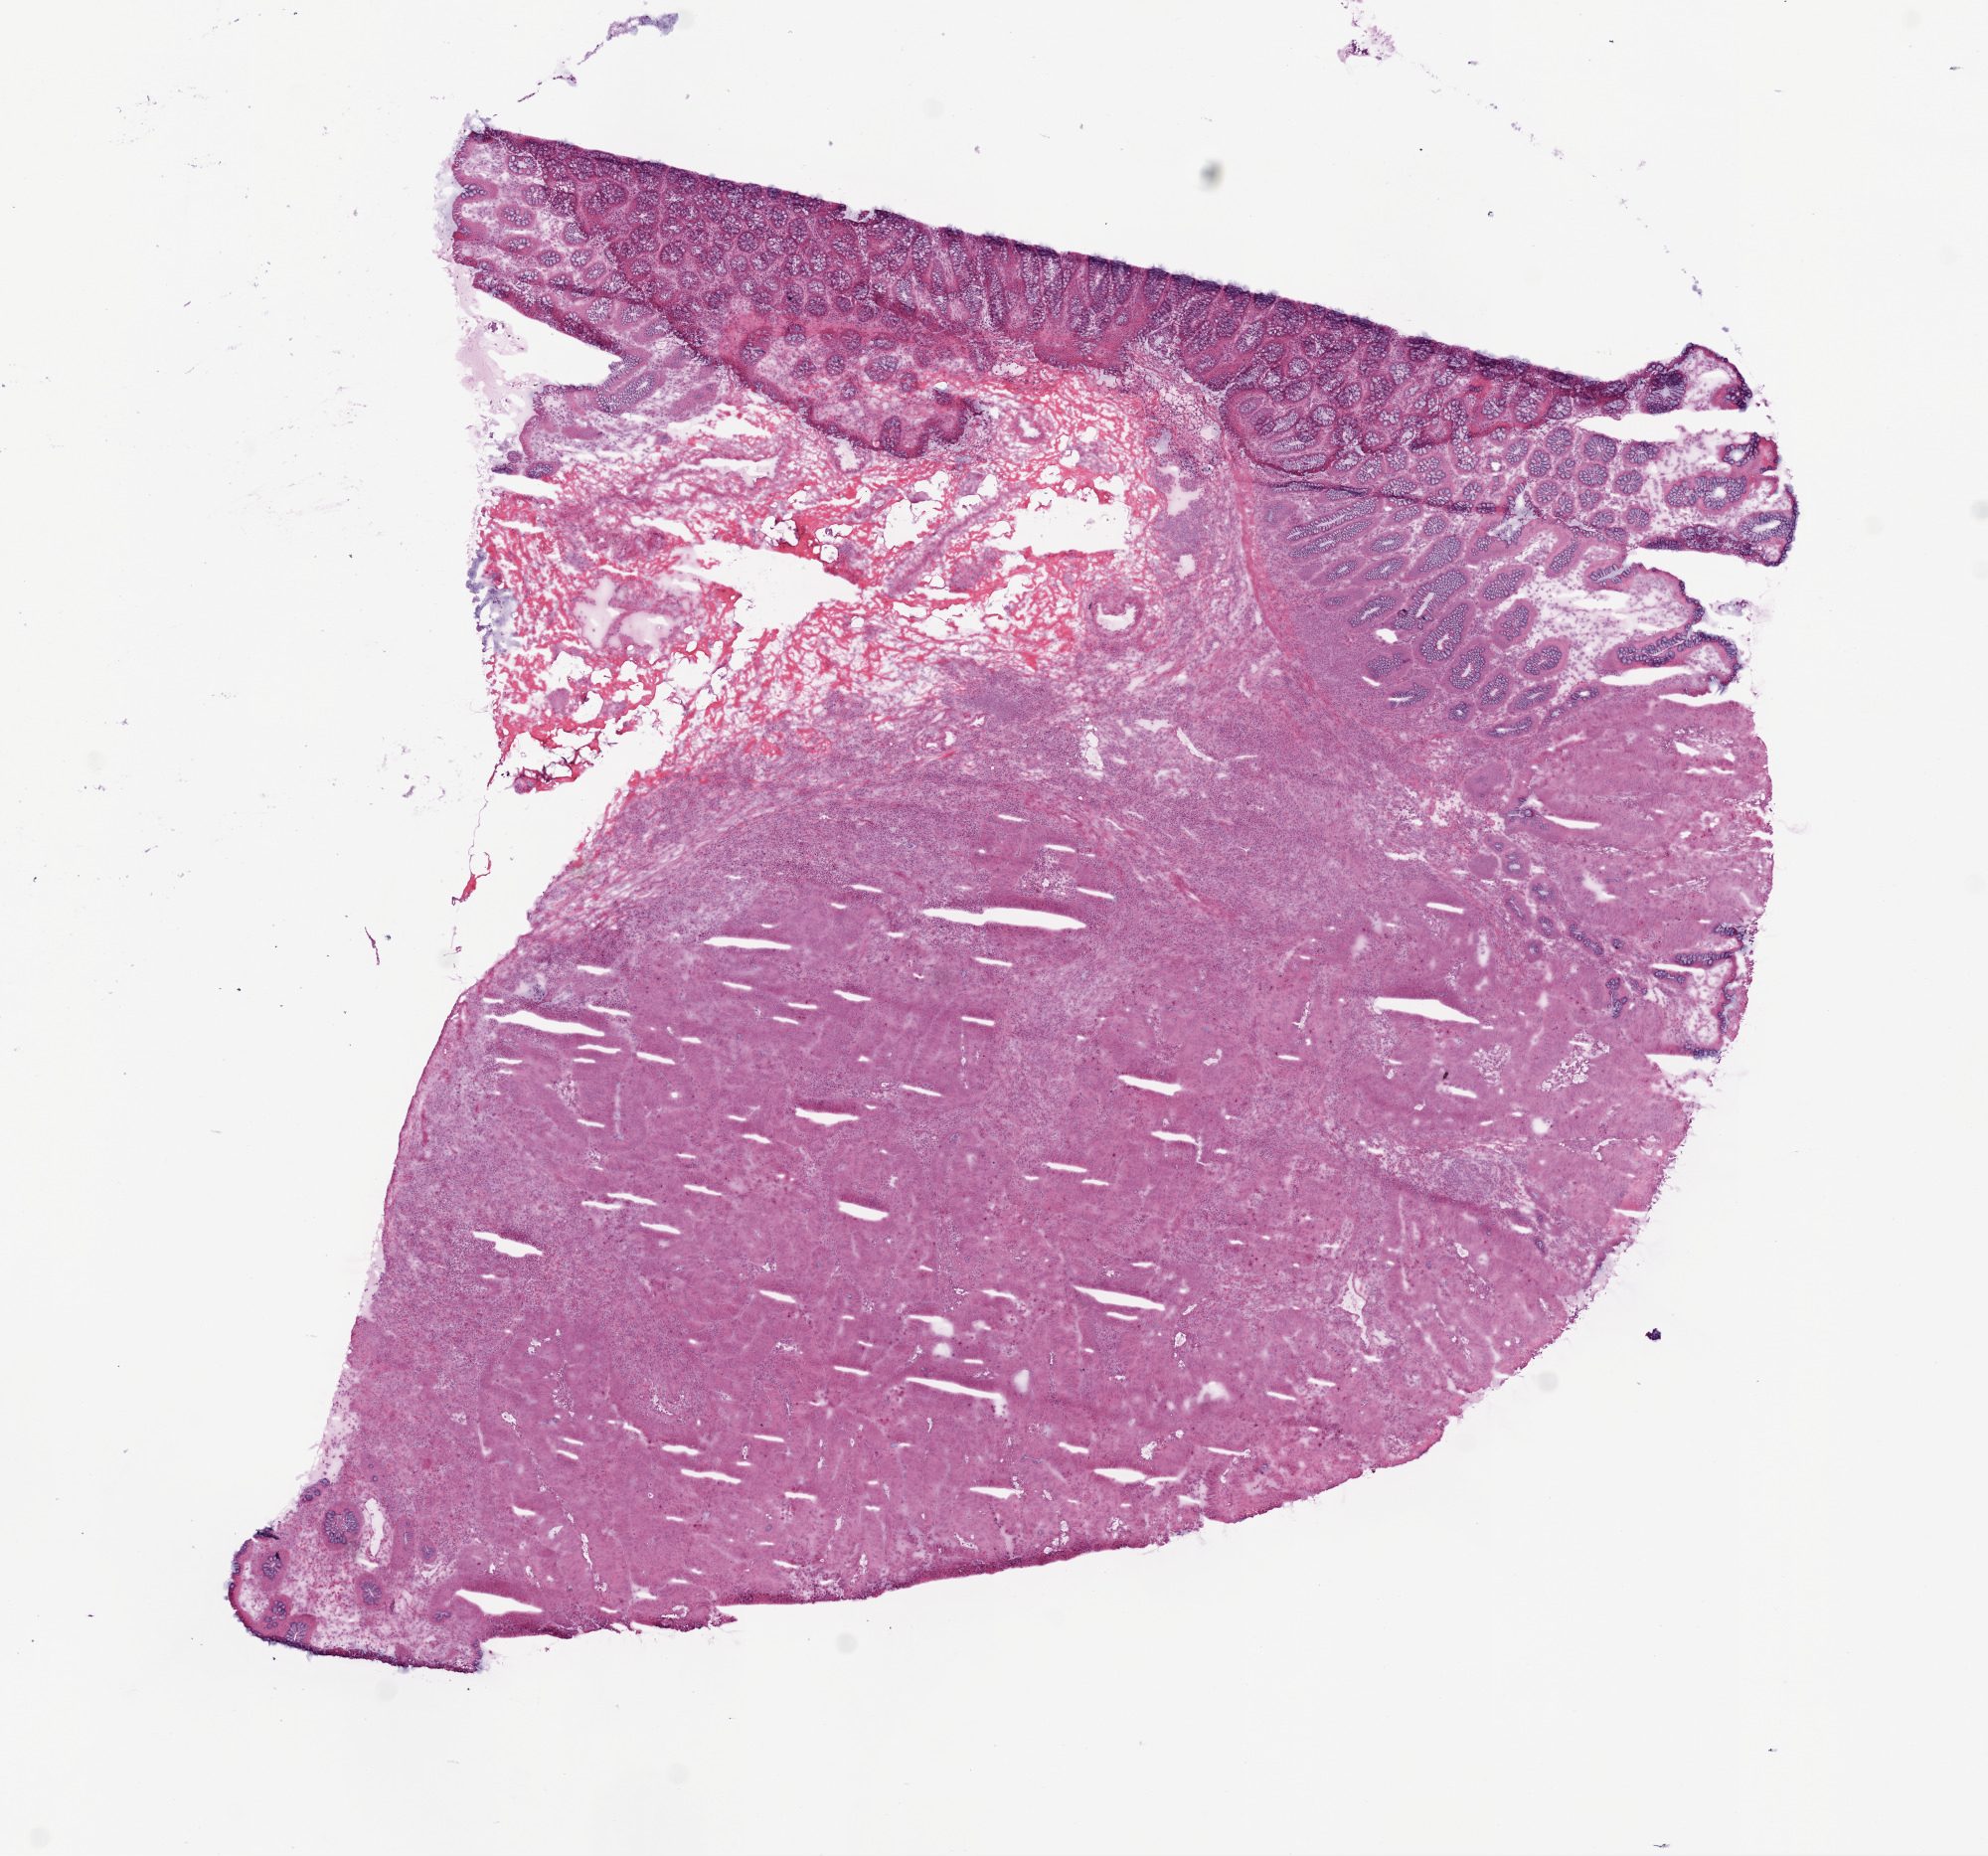
H&E whole-slide image — low-resolution overview of the scanned area, about 8.0 x 7.5 mm (acquisition: 20x scan); frozen section from the bottom of the tissue portion; sample: primary tumour, colon. Patient: female, age at initial diagnosis 78 years. Composition of this section per pathologist review: tumour cells 70%, tumour nuclei 70%, normal cells 15%, stromal cells 10%, necrosis 5%.
Pathologic diagnosis: Adenocarcinoma, NOS (ascending colon). AJCC pathologic stage: I (6th edition). Lymph nodes positive (case pathology): 0 of 31 examined.